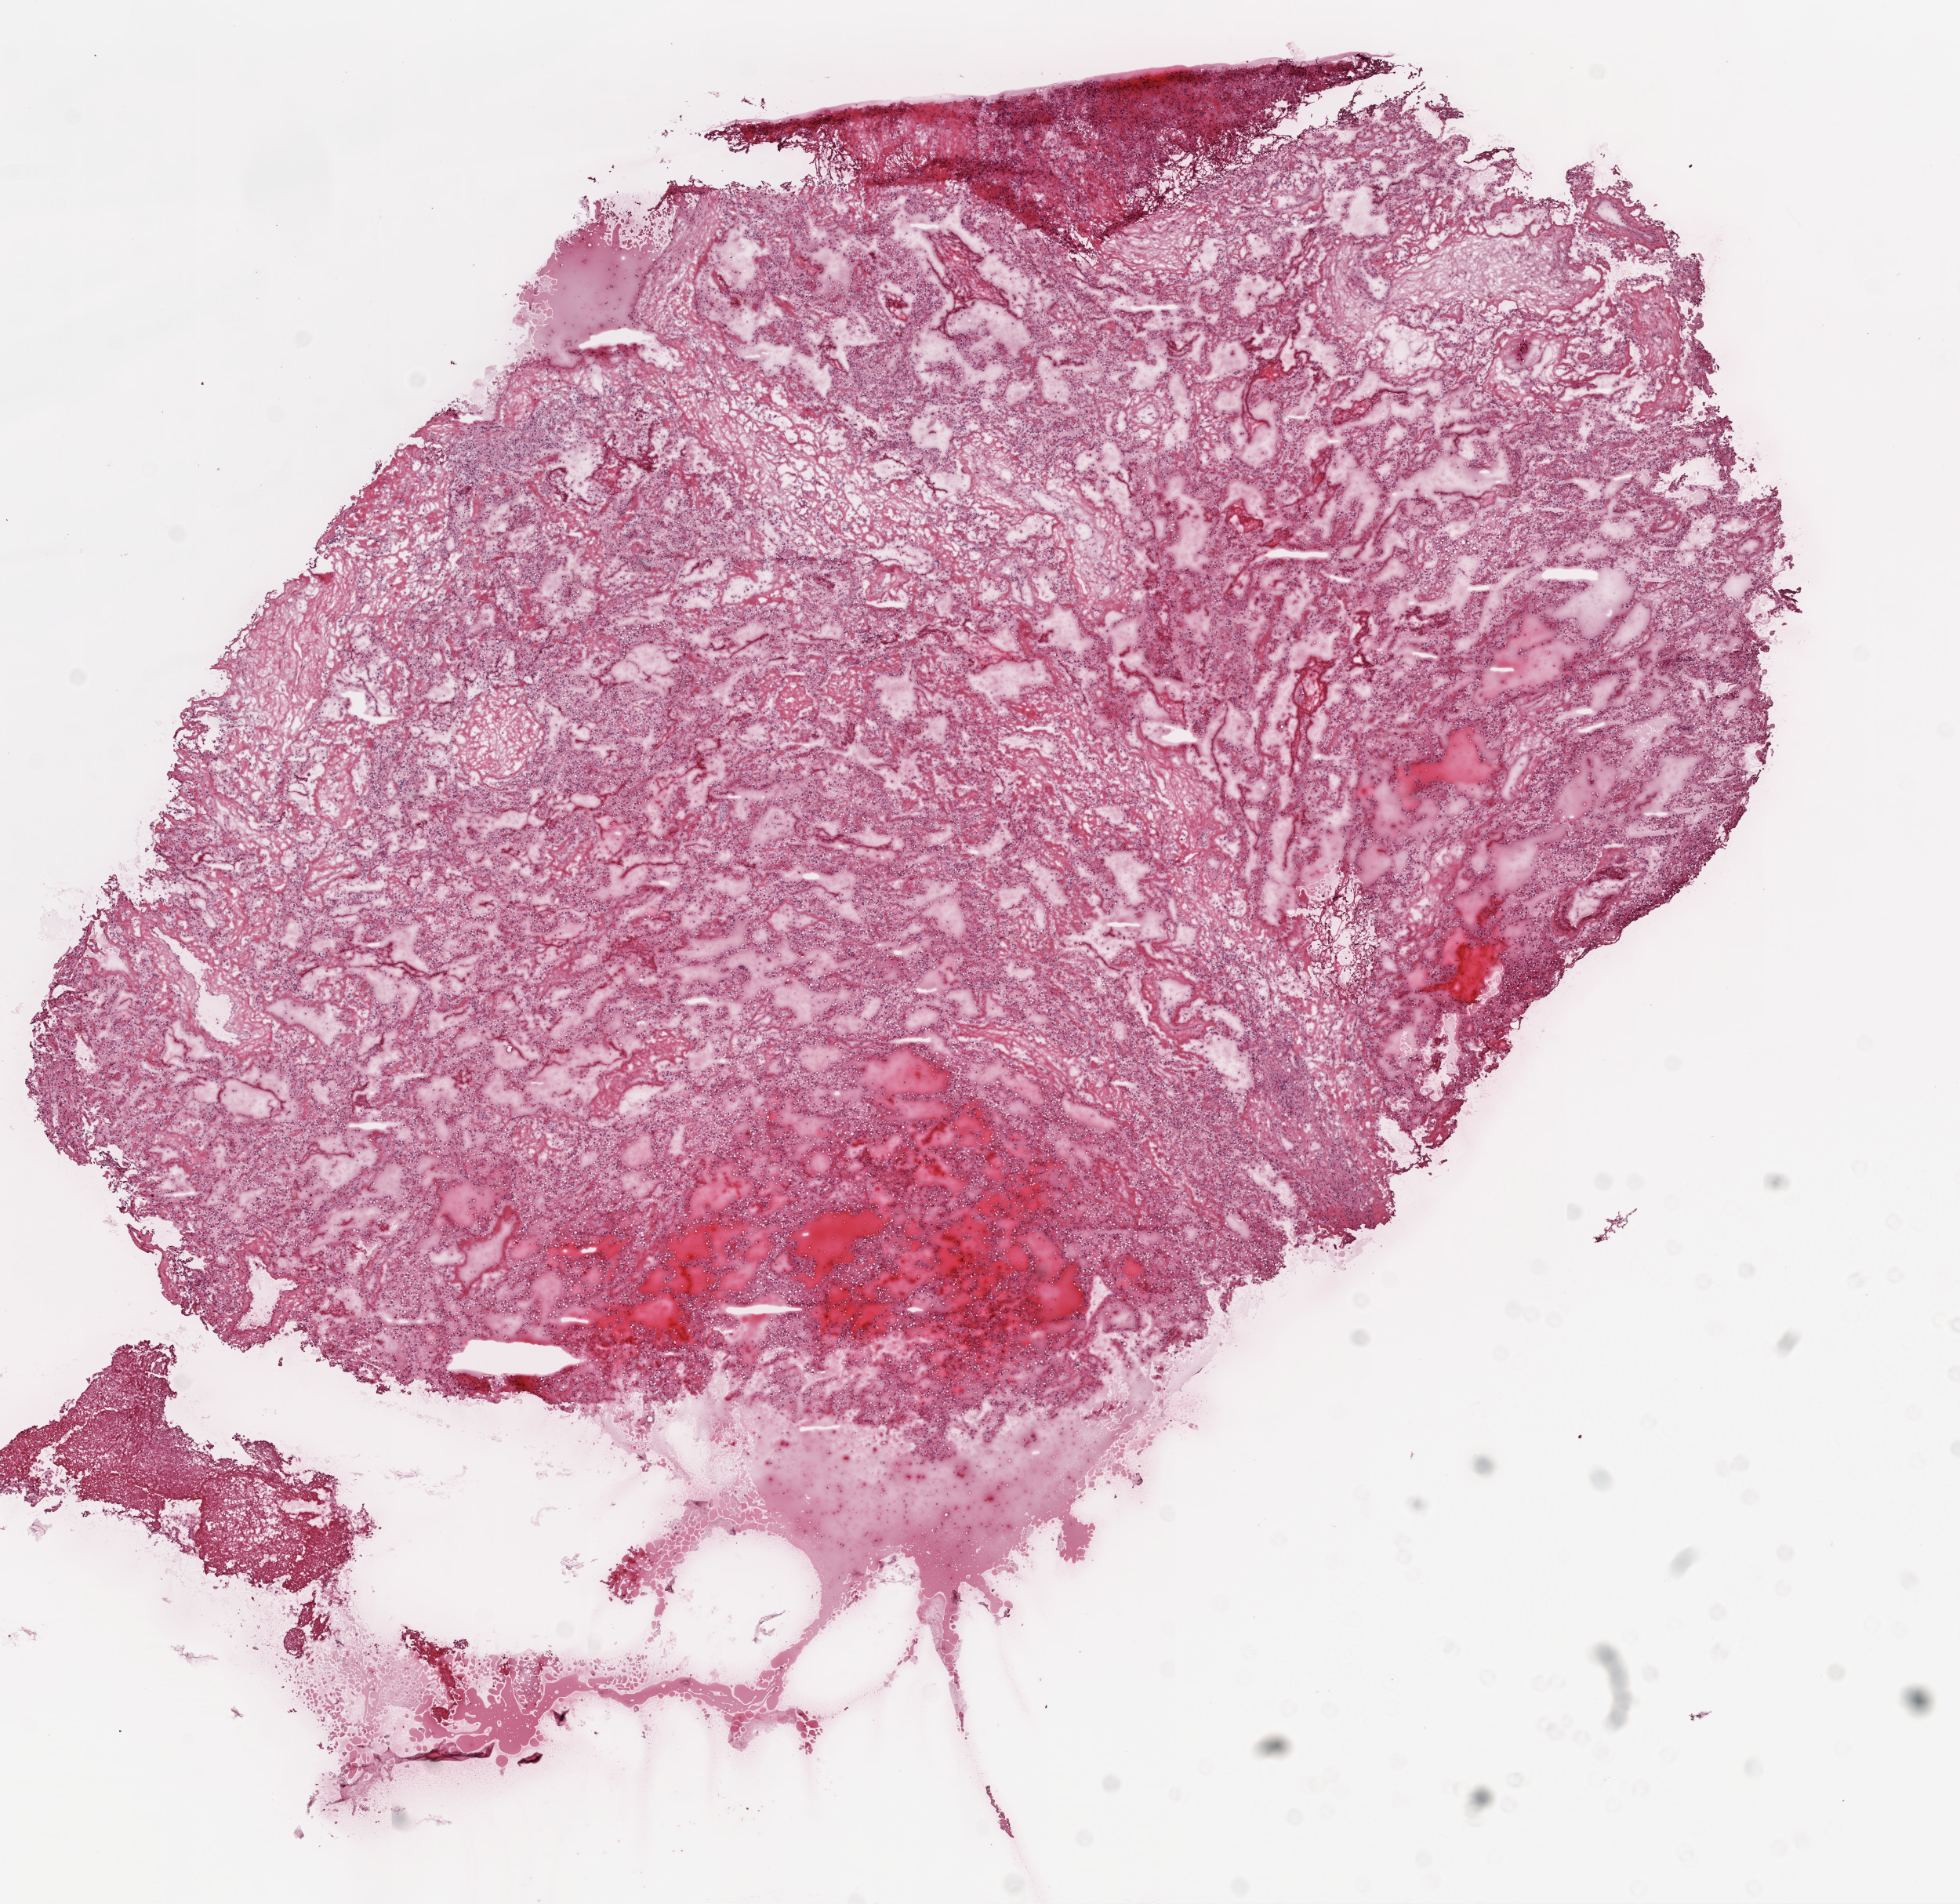
Digitized H&E-stained tissue section (whole slide) — low-resolution overview of the scanned area, about 10.0 x 9.7 mm; frozen section from the top of the tissue portion; primary tumour sample from the kidney. Male patient; age at initial diagnosis 70 years. Histologic grade: G3 (poorly differentiated). Slide review estimates, as recorded: tumour cells 95%, tumour nuclei 95%, normal cells 0%, stromal cells 0%, necrosis 5%.
AJCC pathologic stage: III. Diagnosis: Clear cell adenocarcinoma, NOS. Lymph nodes positive (case pathology): 0 of 2 examined.